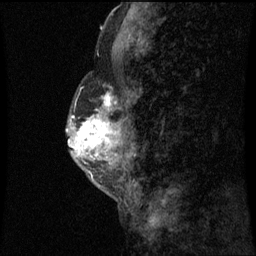
Breast MRI (dynamic contrast-enhanced), one sagittal slice. Slice 25 of 60 in the series (ordered by position). Dynamic contrast-enhanced series, image 2 of 3 at this slice position (ordered by acquisition). 1.5 T. TE 4.2 ms, TR 8.9 ms. 2 mm slice thickness. 256 × 256 image matrix. Female patient, age 50 years. From the clinical record (not read from this slice): setting: breast cancer imaged before/during neoadjuvant chemotherapy; receptor status: triple-negative.
Annotated regions visible in this slice (semi-automatically segmented with operator editing):
- analysis volume of interest (the breast-tissue region the enhancement analysis was run in; not a lesion): box from (x=68, y=86) to (x=116, y=169) px
- tumour enhancement mask (voxels above the 70 % enhancement threshold inside the analysis volume of interest): (x=71, y=94)–(x=113, y=155)